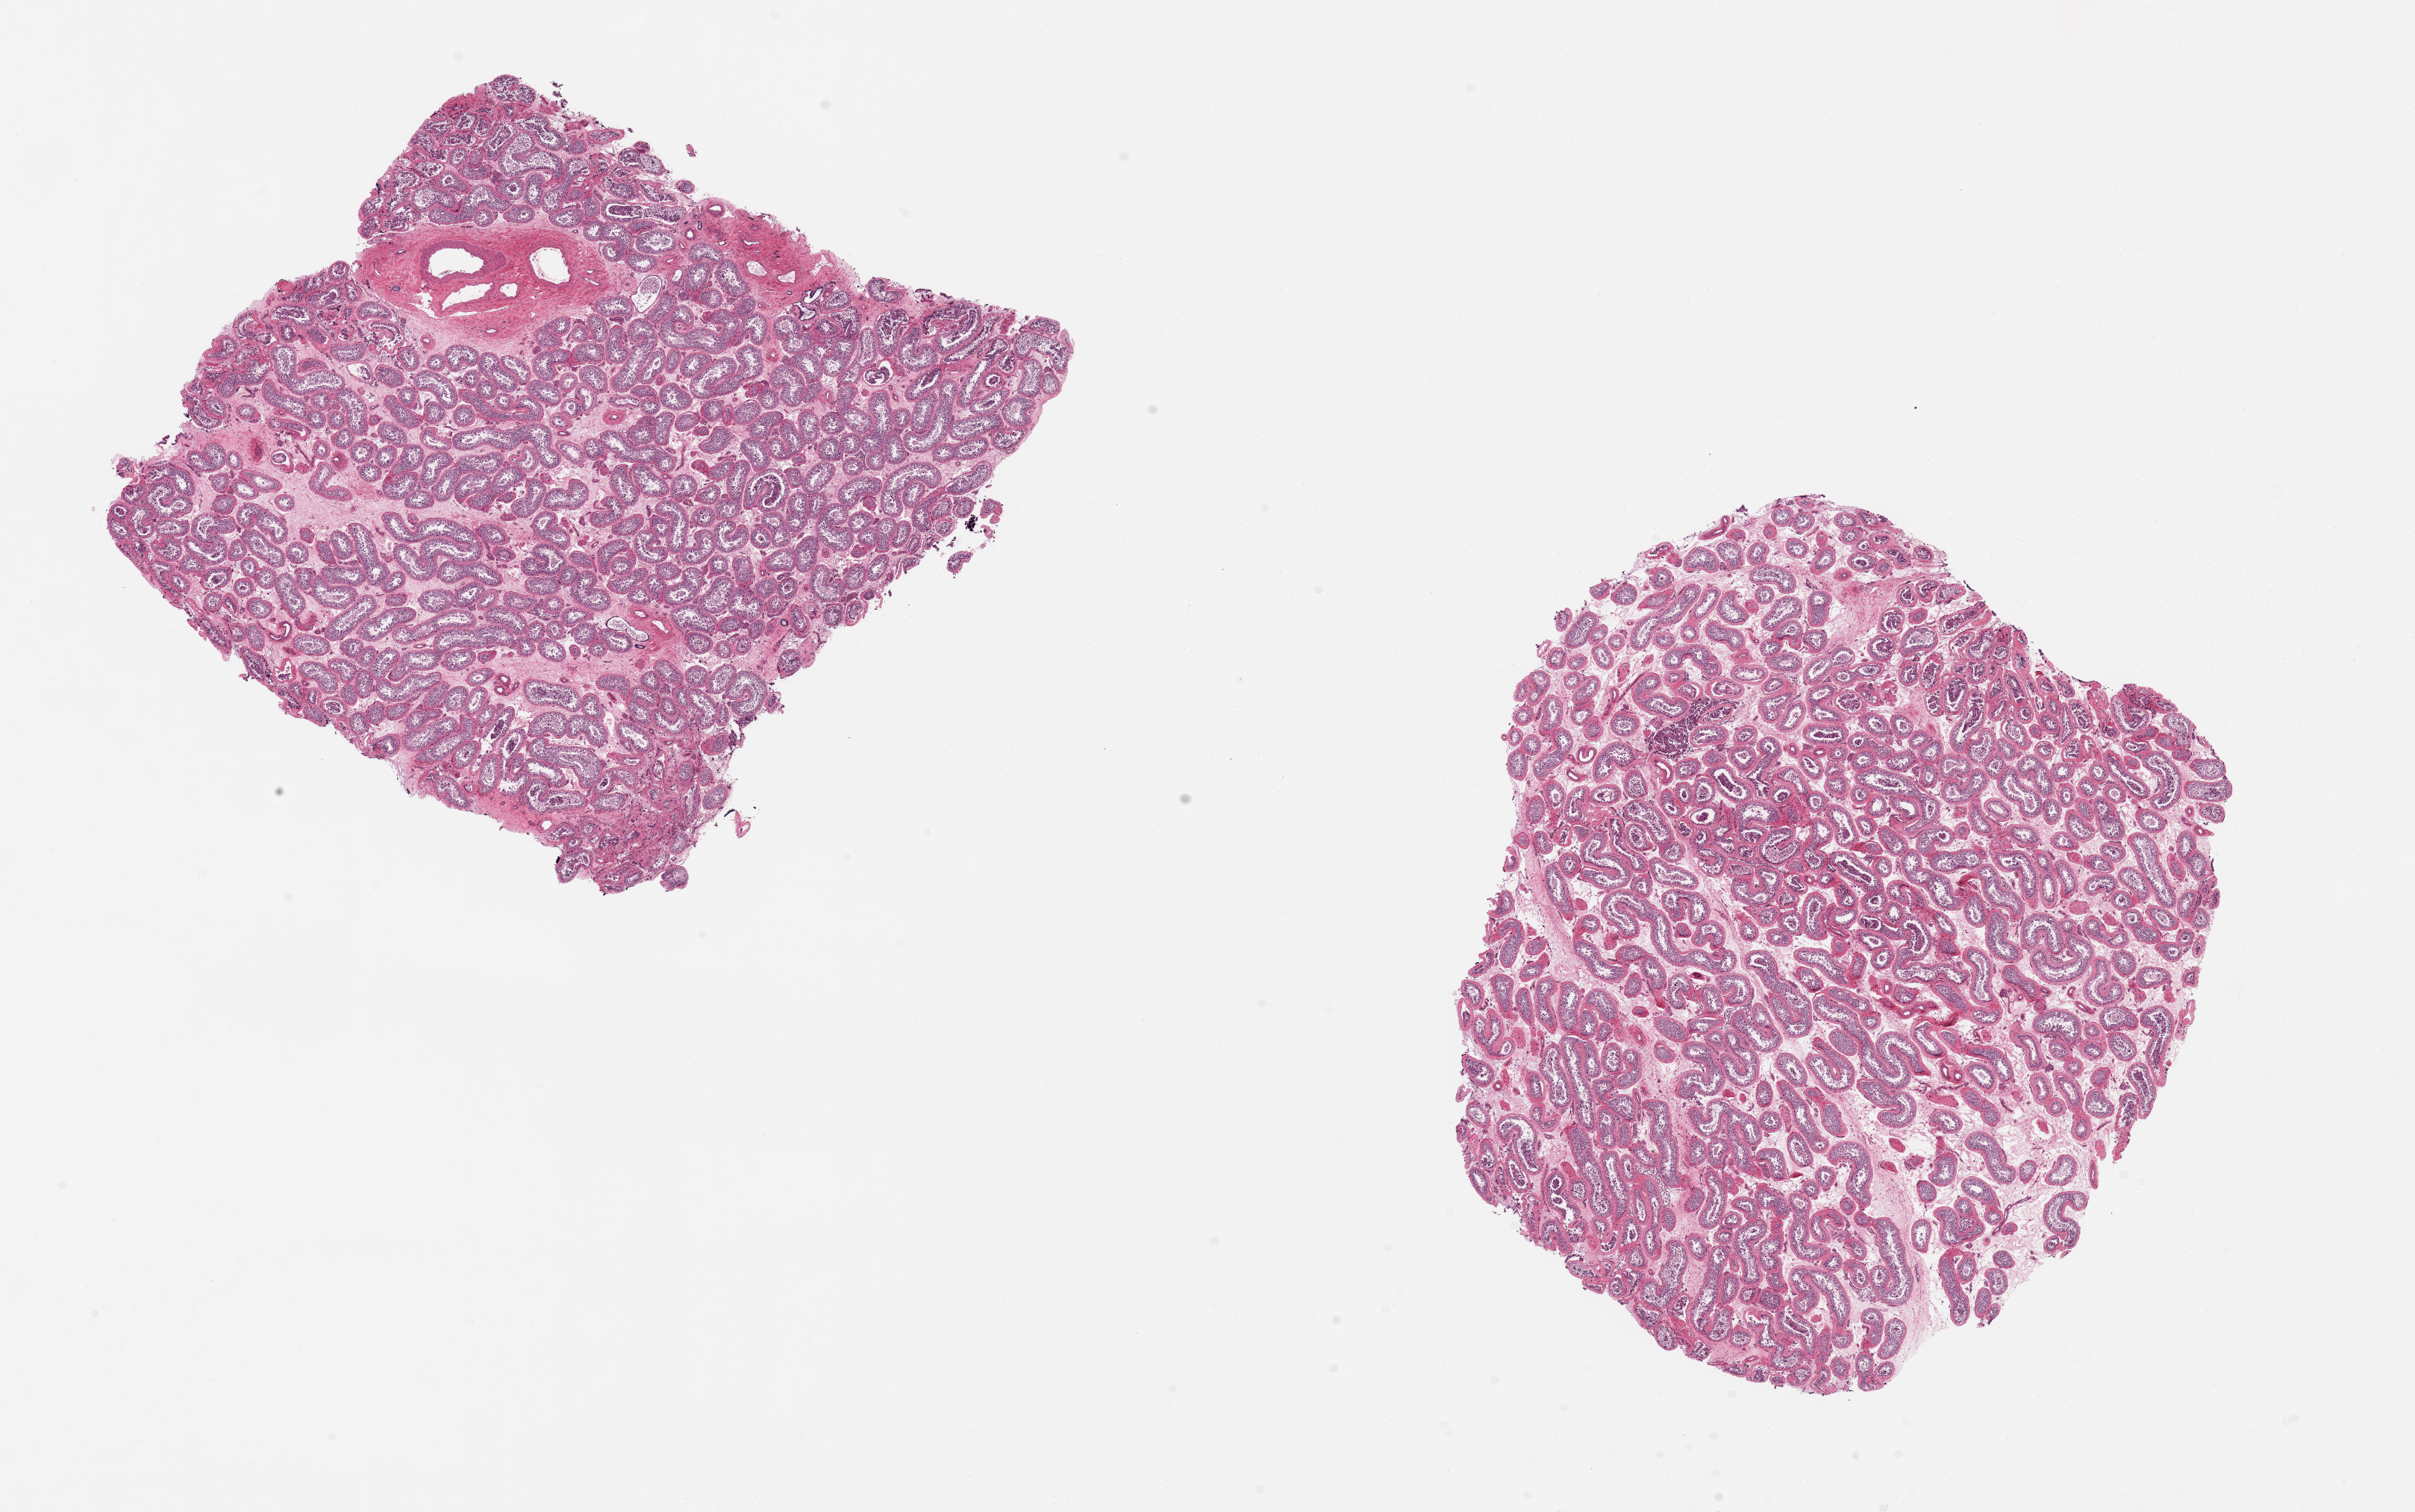
Digitized haematoxylin and eosin-stained section, shown as a low-resolution overview of the whole scanned area (about 25.6 x 16.0 mm), PAXgene-fixed, paraffin-embedded tissue, section of testis (target tissue), tissue donor sample. Male donor.
Reviewer comment on this tissue sample: 2 ~7.5x7mm pieces, good sperm maturation evident.